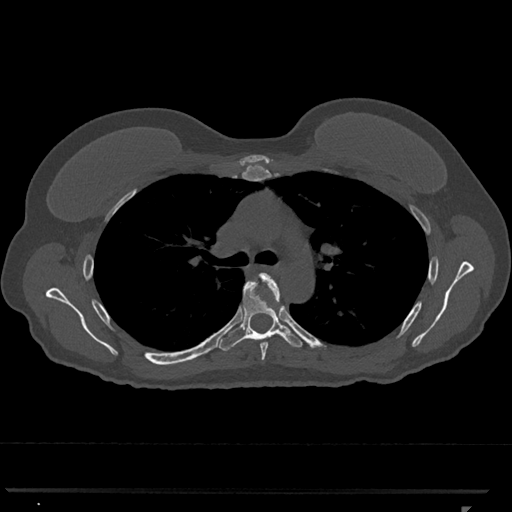
CT including the spine, one axial slice. Position 779 of 793 along the scan axis. Reconstruction kernel Br40s/3. Bone window (W 1800 / L 400 HU). 0.5 mm slice thickness. 512 × 512 image matrix, field of view 380 × 380 mm. Female patient, age 62 years. From the clinical record (not read from this slice): primary cancer: renal.
Structures marked on this image (semi-automatic segmentation, software-assisted and operator-edited):
- T5 vertebra: box from (x=259, y=273) to (x=281, y=360) px
- T6 vertebra: (x=219, y=279)–(x=303, y=351)